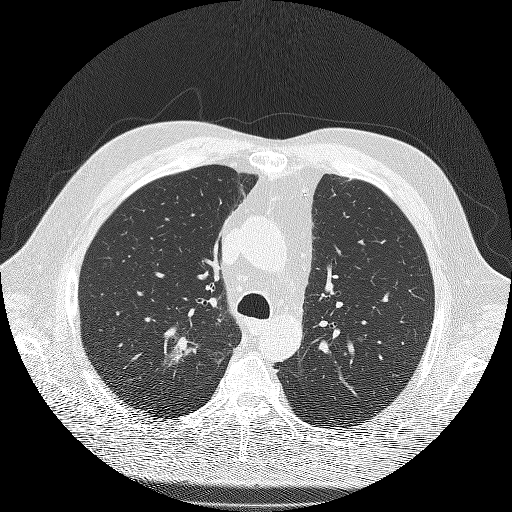
Low-dose screening chest CT, one axial slice. Position 139 of 180 along the scan axis. Reconstruction kernel FC51. 120 kVp. Lung window (W 1500 / L -600 HU). 2 mm slice thickness. 512 × 512 image matrix.
Structures marked on this image (expert manual segmentation):
- lesion 1 (tumor, upper lobe of right lung): bounding box [x1, y1, x2, y2] px = [168, 337, 197, 366]